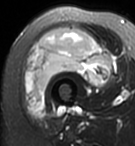
MRI of an extremity soft-tissue mass, one axial slice; slice 35 of 95 in the series (ordered by position); T2-weighted fat-saturated; MR volume resampled by the dataset authors to the PET/CT grid (not the native acquisition matrix); 135 × 146 image matrix, field of view 132 × 143 mm. Female patient. From the clinical record (not read from this slice): histological type: pleiomorphic undifferentiated sarcoma; grade: high; site of the primary tumour: right quadricep.
Annotated regions visible in this slice (expert contour drawn on MRI and transferred to this co-registered scan by the dataset authors):
- gross tumour volume including surrounding oedema: bounding box [x1, y1, x2, y2] px = [25, 29, 111, 114]
- gross tumour volume (mass): [25, 29, 111, 114]